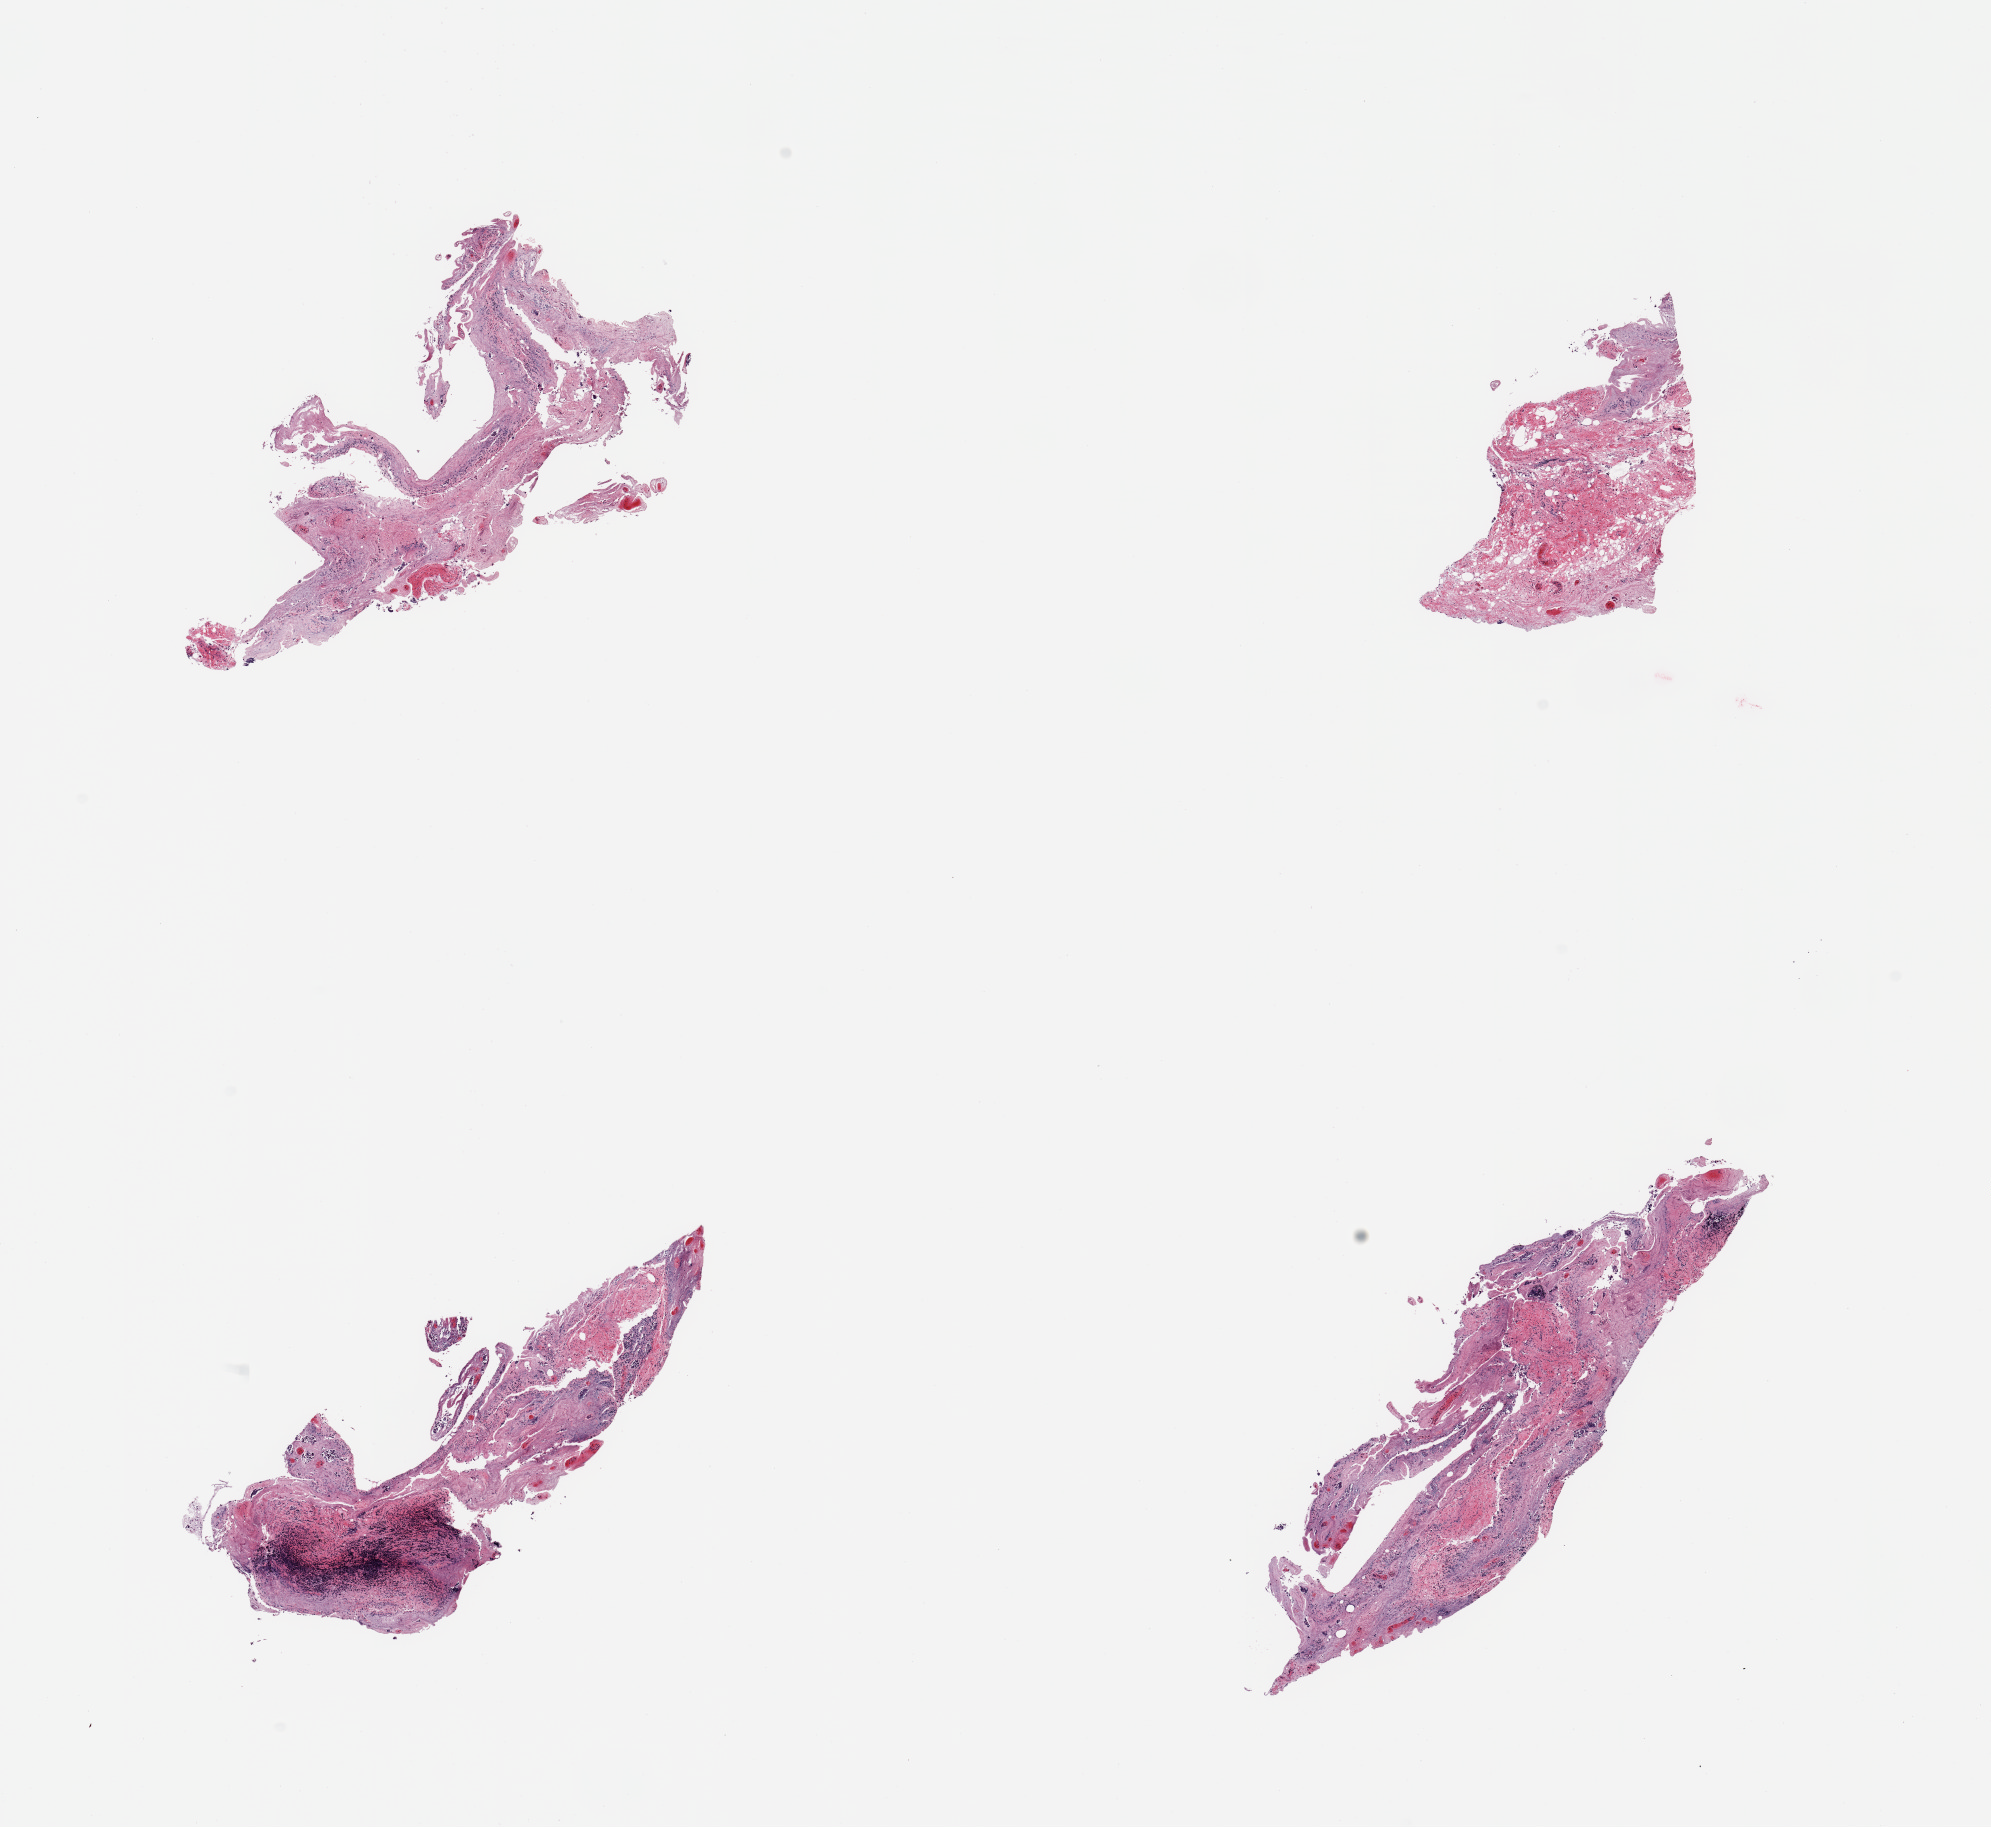
Digitized hematoxylin and eosin (H&E)-stained section — low-resolution overview of the scanned area, about 15.8 x 14.5 mm; PAXgene-fixed paraffin-embedded (PFPE) section; target tissue: ileum; donor tissue sample.
Review note (as recorded): 4 pieces; autolyzed mucosa with minimal residual lymphoid tissue.